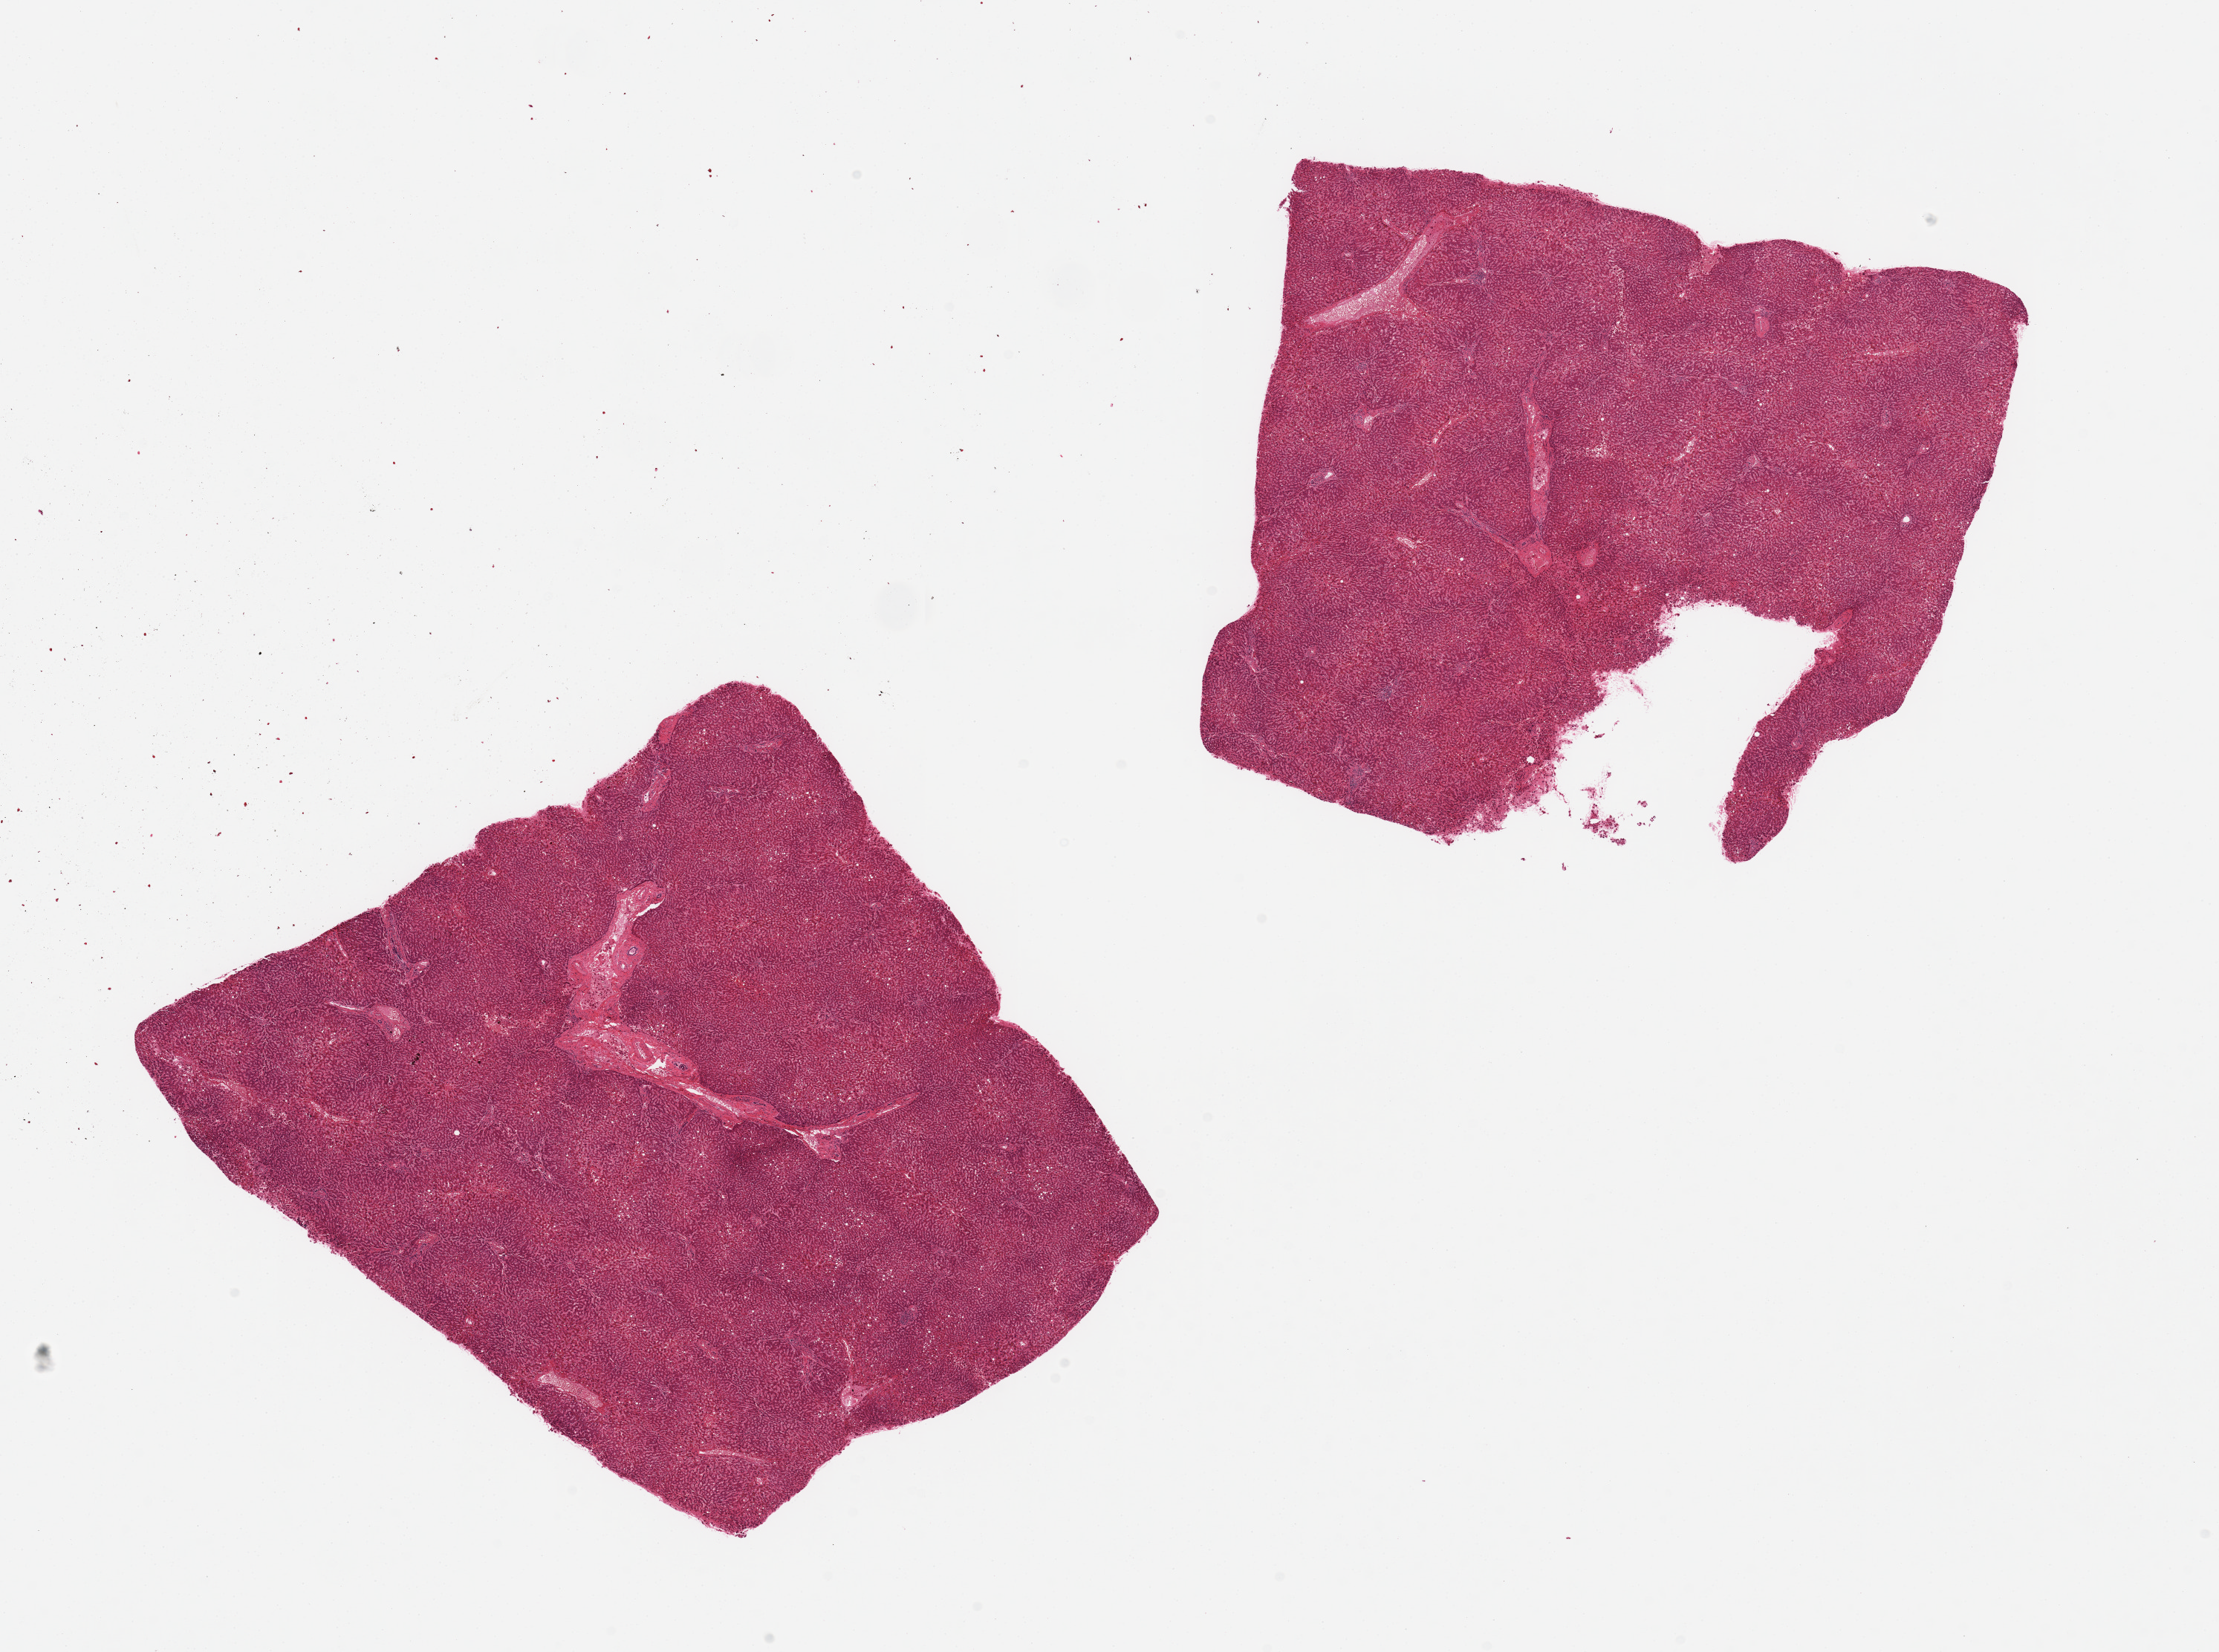
H&E whole-slide image — a low-resolution overview of the entire scanned area, about 23.6 x 17.6 mm (slide scanned at 20x), PAXgene-fixed paraffin-embedded (PFPE) section, section of liver (target tissue), donor tissue sample. Male donor.
* pathologist's review note for this sample: 2 pieces; <10% macrovesicular fat